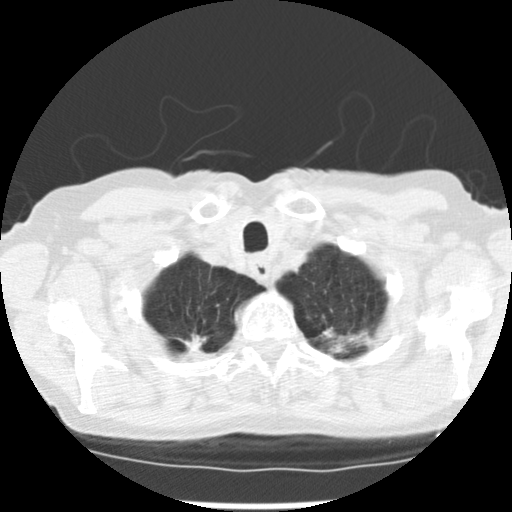
Axial slice from a low-dose chest CT screening exam. Baseline annual screen. Lung window (W 1500 / L -600 HU). 2.5 mm slice thickness. Slice 20 of 265 in the series. Female, age 72 years at enrolment.
Lesion marked by an expert reader, bounding box (x1, y1, x2, y2) in pixels: (165, 317, 231, 365). The screening reader recorded 3 non-calcified nodules or masses ≥4 mm on this exam; which of them this box marks is not recorded. Official screen result: positive, change unspecified: nodule(s) >= 4 mm or enlarging nodule(s), mass(es), or other non-specific abnormalities suspicious for lung cancer.